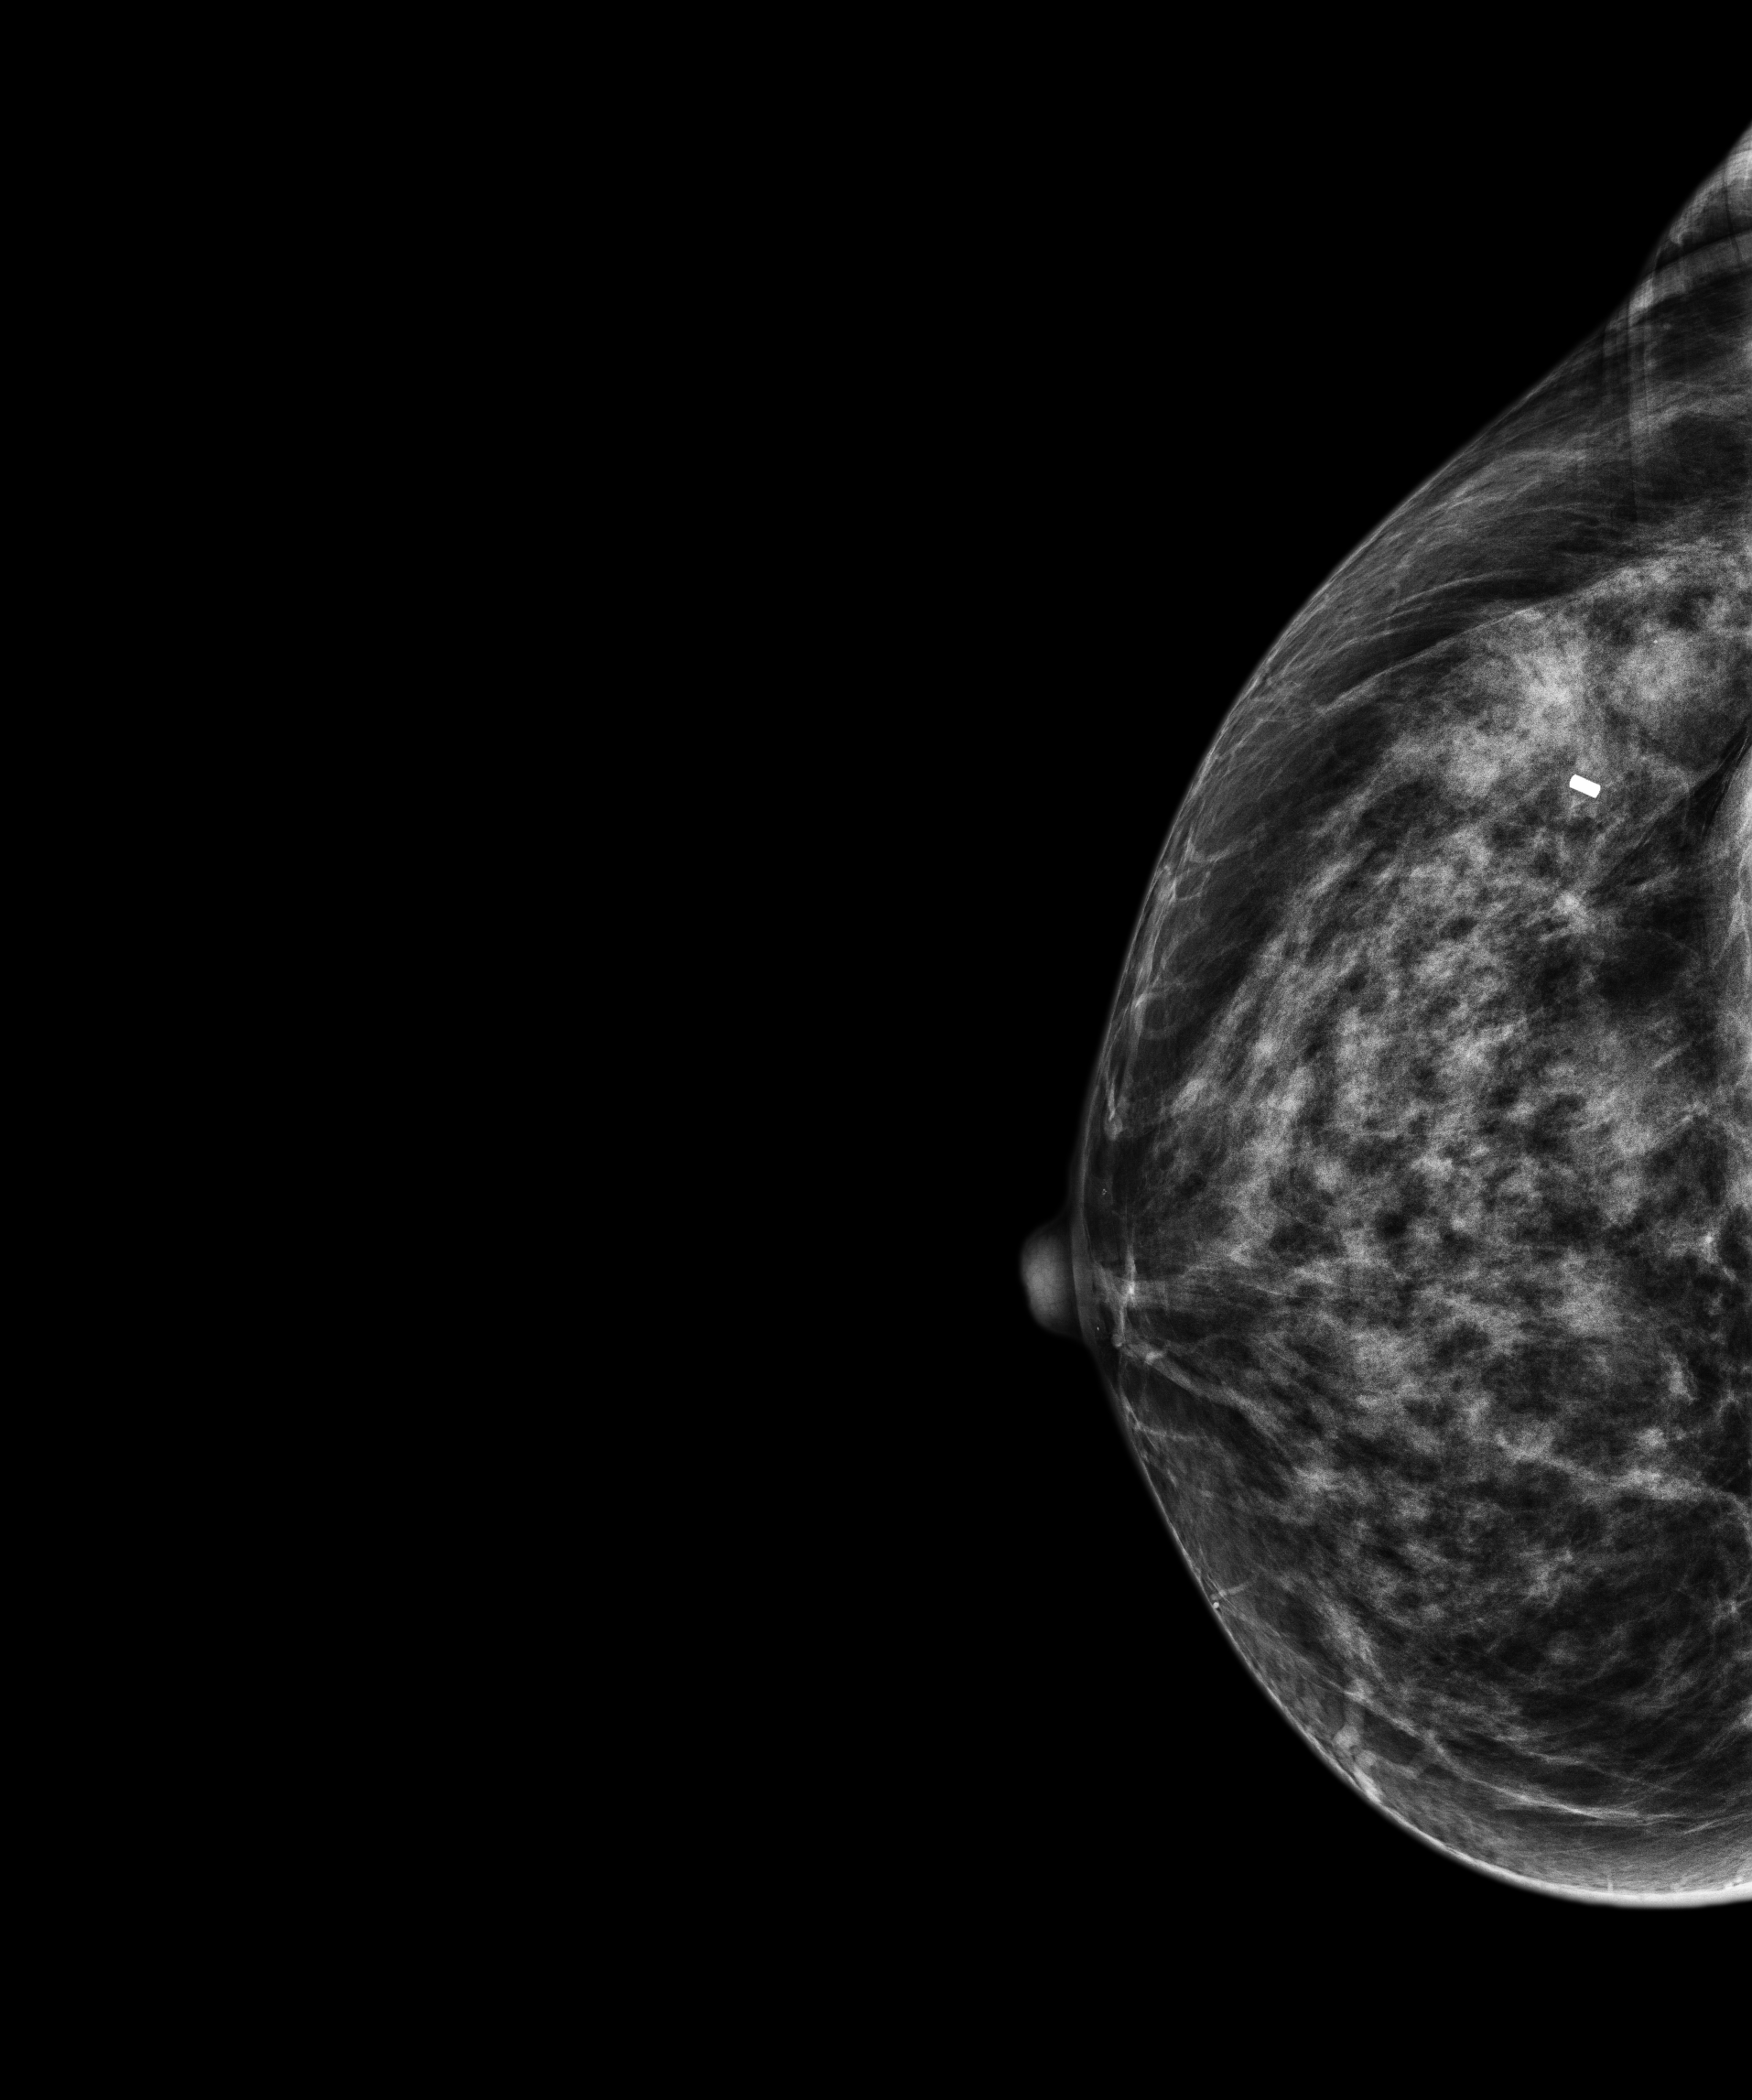
Screening examination, compressed breast thickness 55.1 mm, system: Senographe Pristina. Patient: female, 57 years.
Image type: full-field digital mammogram. Breast: right. Projection: craniocaudal (CC) view.